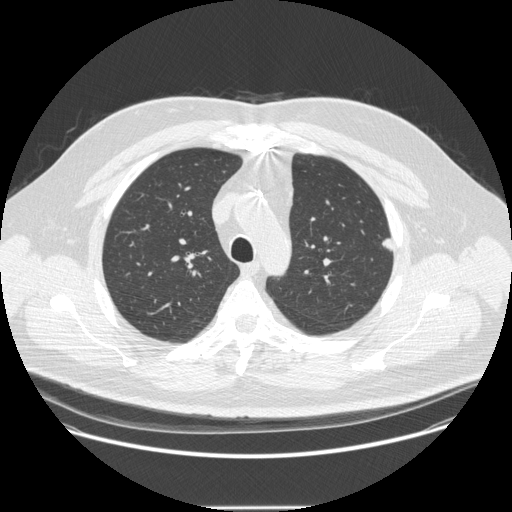
Chest CT (low-dose screening protocol), one axial image, second annual screen, lung window (W 1500 / L -600 HU), 120 kVp, slice 72 of 251 in the series. Male participant, aged 55 years at enrolment. Former smoker at enrolment.
• Expert-annotated lung lesion, box from (x=373, y=230) to (x=405, y=251) px.
• The screening reader recorded 2 non-calcified nodules or masses ≥4 mm on this exam (left upper lobe, left upper lobe); which of them this box marks is not recorded.
• Participant outcome: lung cancer diagnosed 60 days after this screen — adenocarcinoma, NOS, left upper lobe, moderately differentiated (G2), stage IA (AJCC 6th edition), 9 mm at pathology.